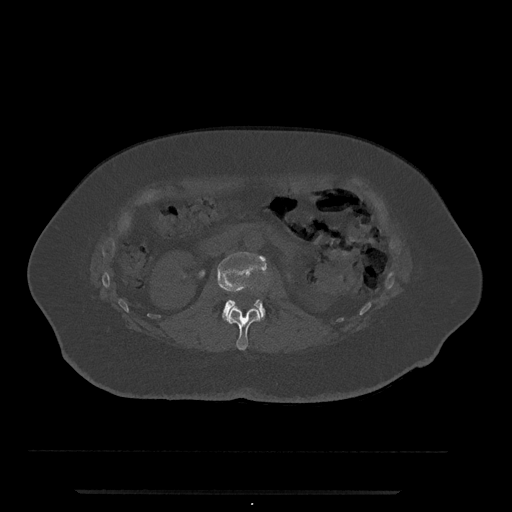
CT including the spine, one axial slice. Slice 68 of 797 in the series (ordered by position). Reconstruction kernel Br40s/3. 120 kVp. Bone window (W 1800 / L 400 HU). 0.5 mm slice thickness. 512 × 512 image matrix, field of view 440 × 440 mm. Female patient, age 51 years. From the clinical record (not read from this slice): primary cancer: neuro; vertebrae with lytic lesions (as recorded): T8.
Structures marked on this image (semi-automatic segmentation, software-assisted and operator-edited):
- L1 vertebra: bounding box [x1, y1, x2, y2] px = [225, 308, 262, 350]
- L2 vertebra: [218, 252, 267, 321]